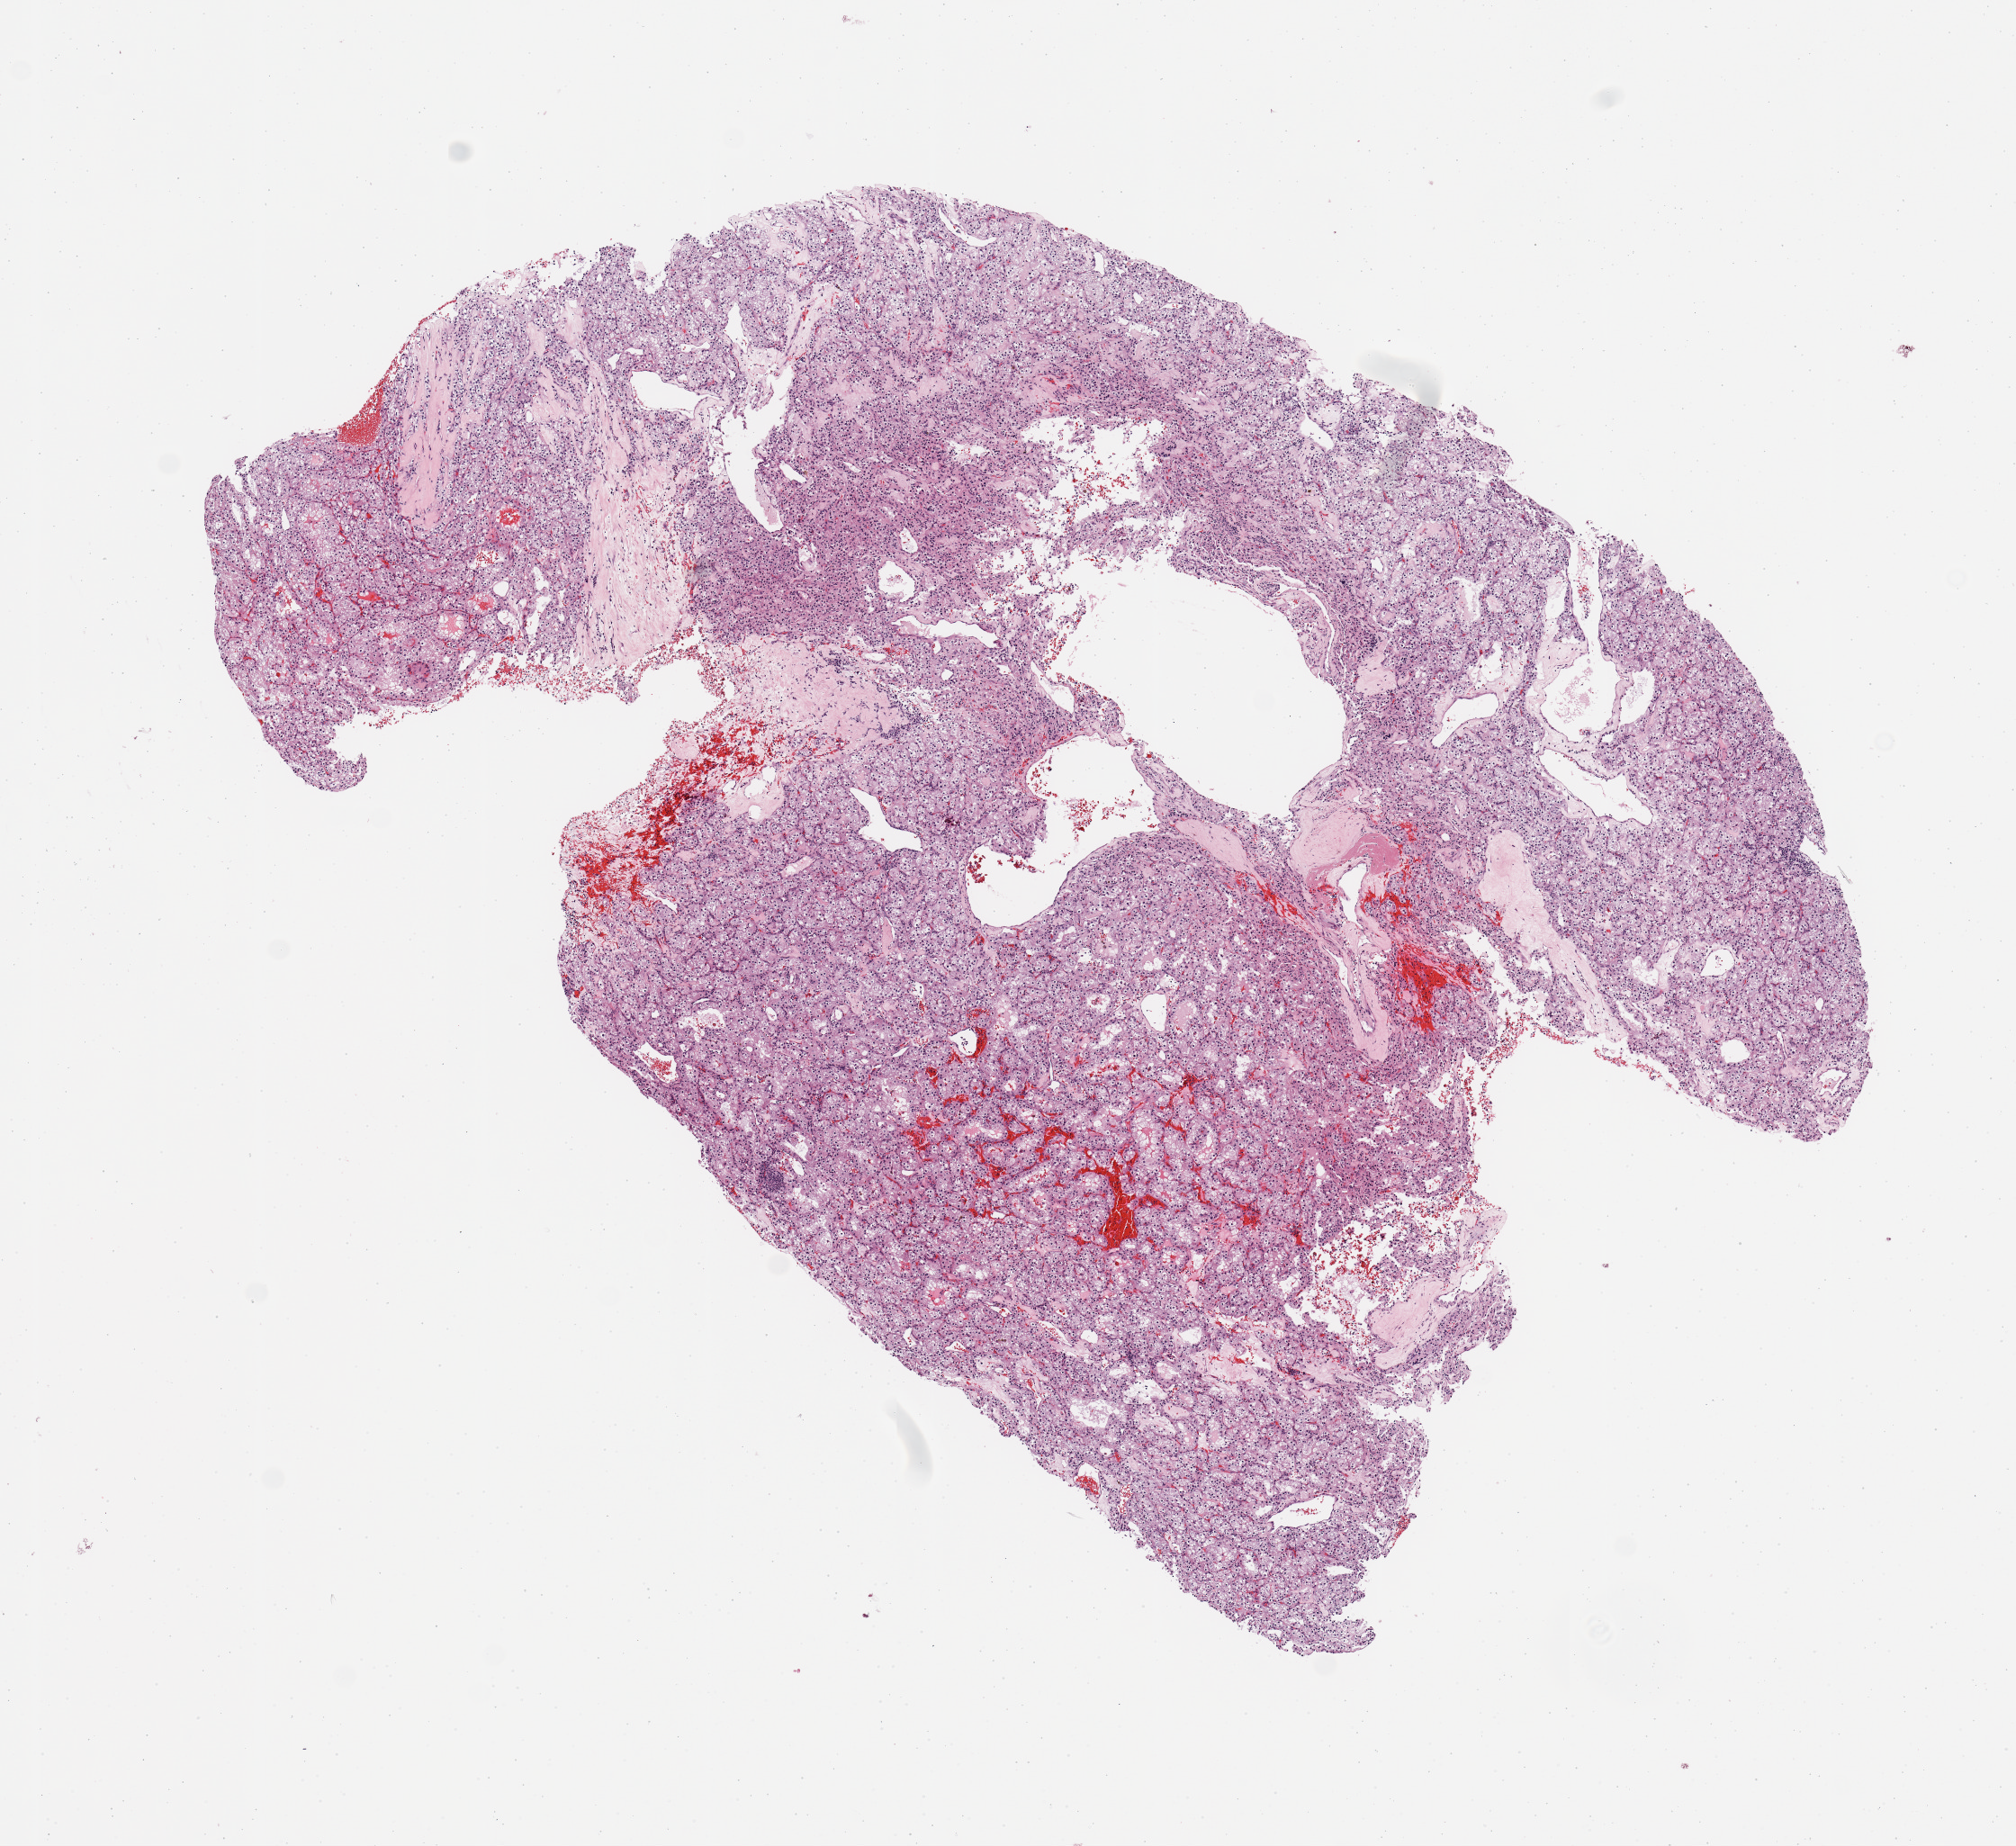
H&E-stained whole-slide image, whole scanned area (about 8.9 x 8.1 mm) shown as a low-resolution overview. Tumour tissue sample, kidney. 72-year-old male patient. Histologic grade: G3 (poorly differentiated).
• AJCC pathologic stage: II
• histologic diagnosis: Renal cell carcinoma, NOS